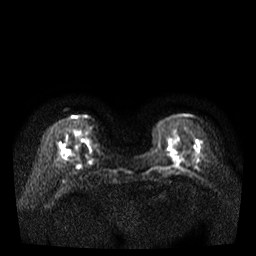
Breast MRI, one axial slice. Position 11 of 35 along the scan axis. Diffusion-weighted series; image 2 of 4 stored at this slice position (different b-values; order by instance number). 3 T. 256 × 256 image matrix. Female patient.
Structures marked on this image (outlined manually by an expert reader):
- tumour on diffusion-weighted imaging: bounding box (x1, y1, x2, y2) in pixels: (171, 151, 178, 161)